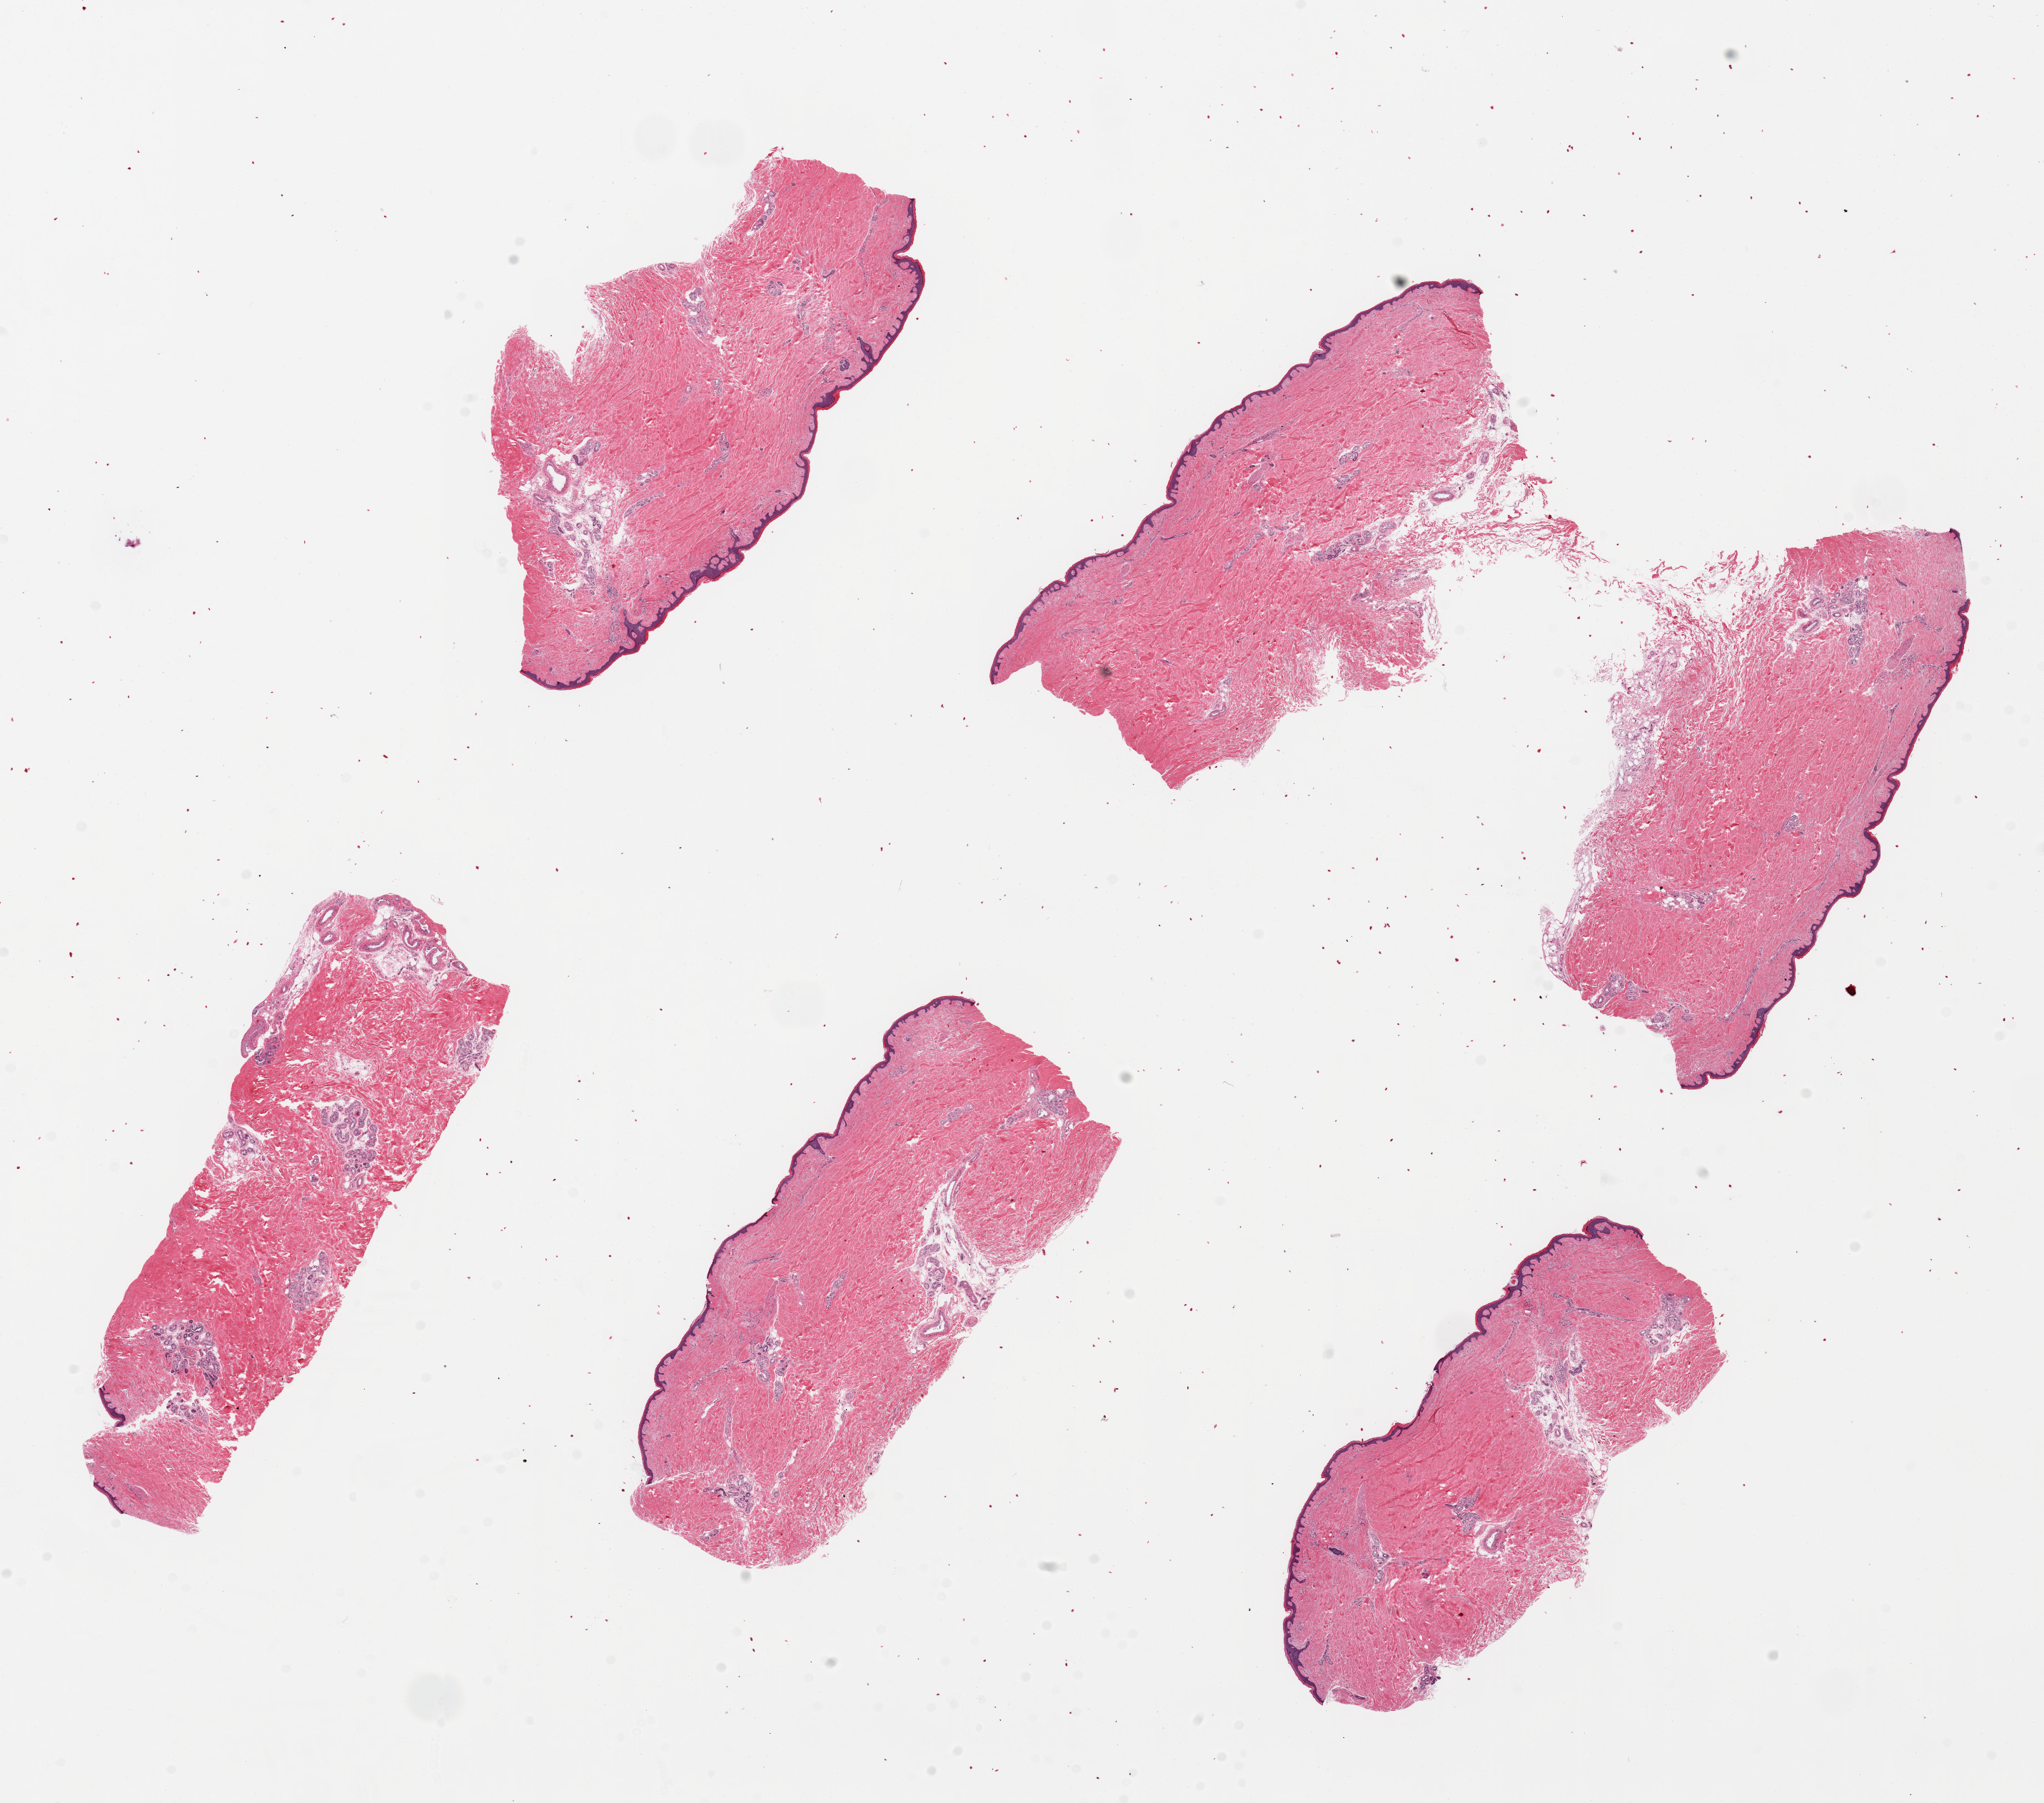
Digitized H&E-stained section — whole scanned area (about 22.6 x 20.0 mm) shown as a low-resolution overview, PAXgene-fixed, paraffin-embedded tissue, section of skin of lower leg (target tissue), tissue donor sample. Female donor.
* reviewer comment on this tissue sample: 6 pieces, up to 7.5x3mm; well trimmed, no subcutaneous adipose